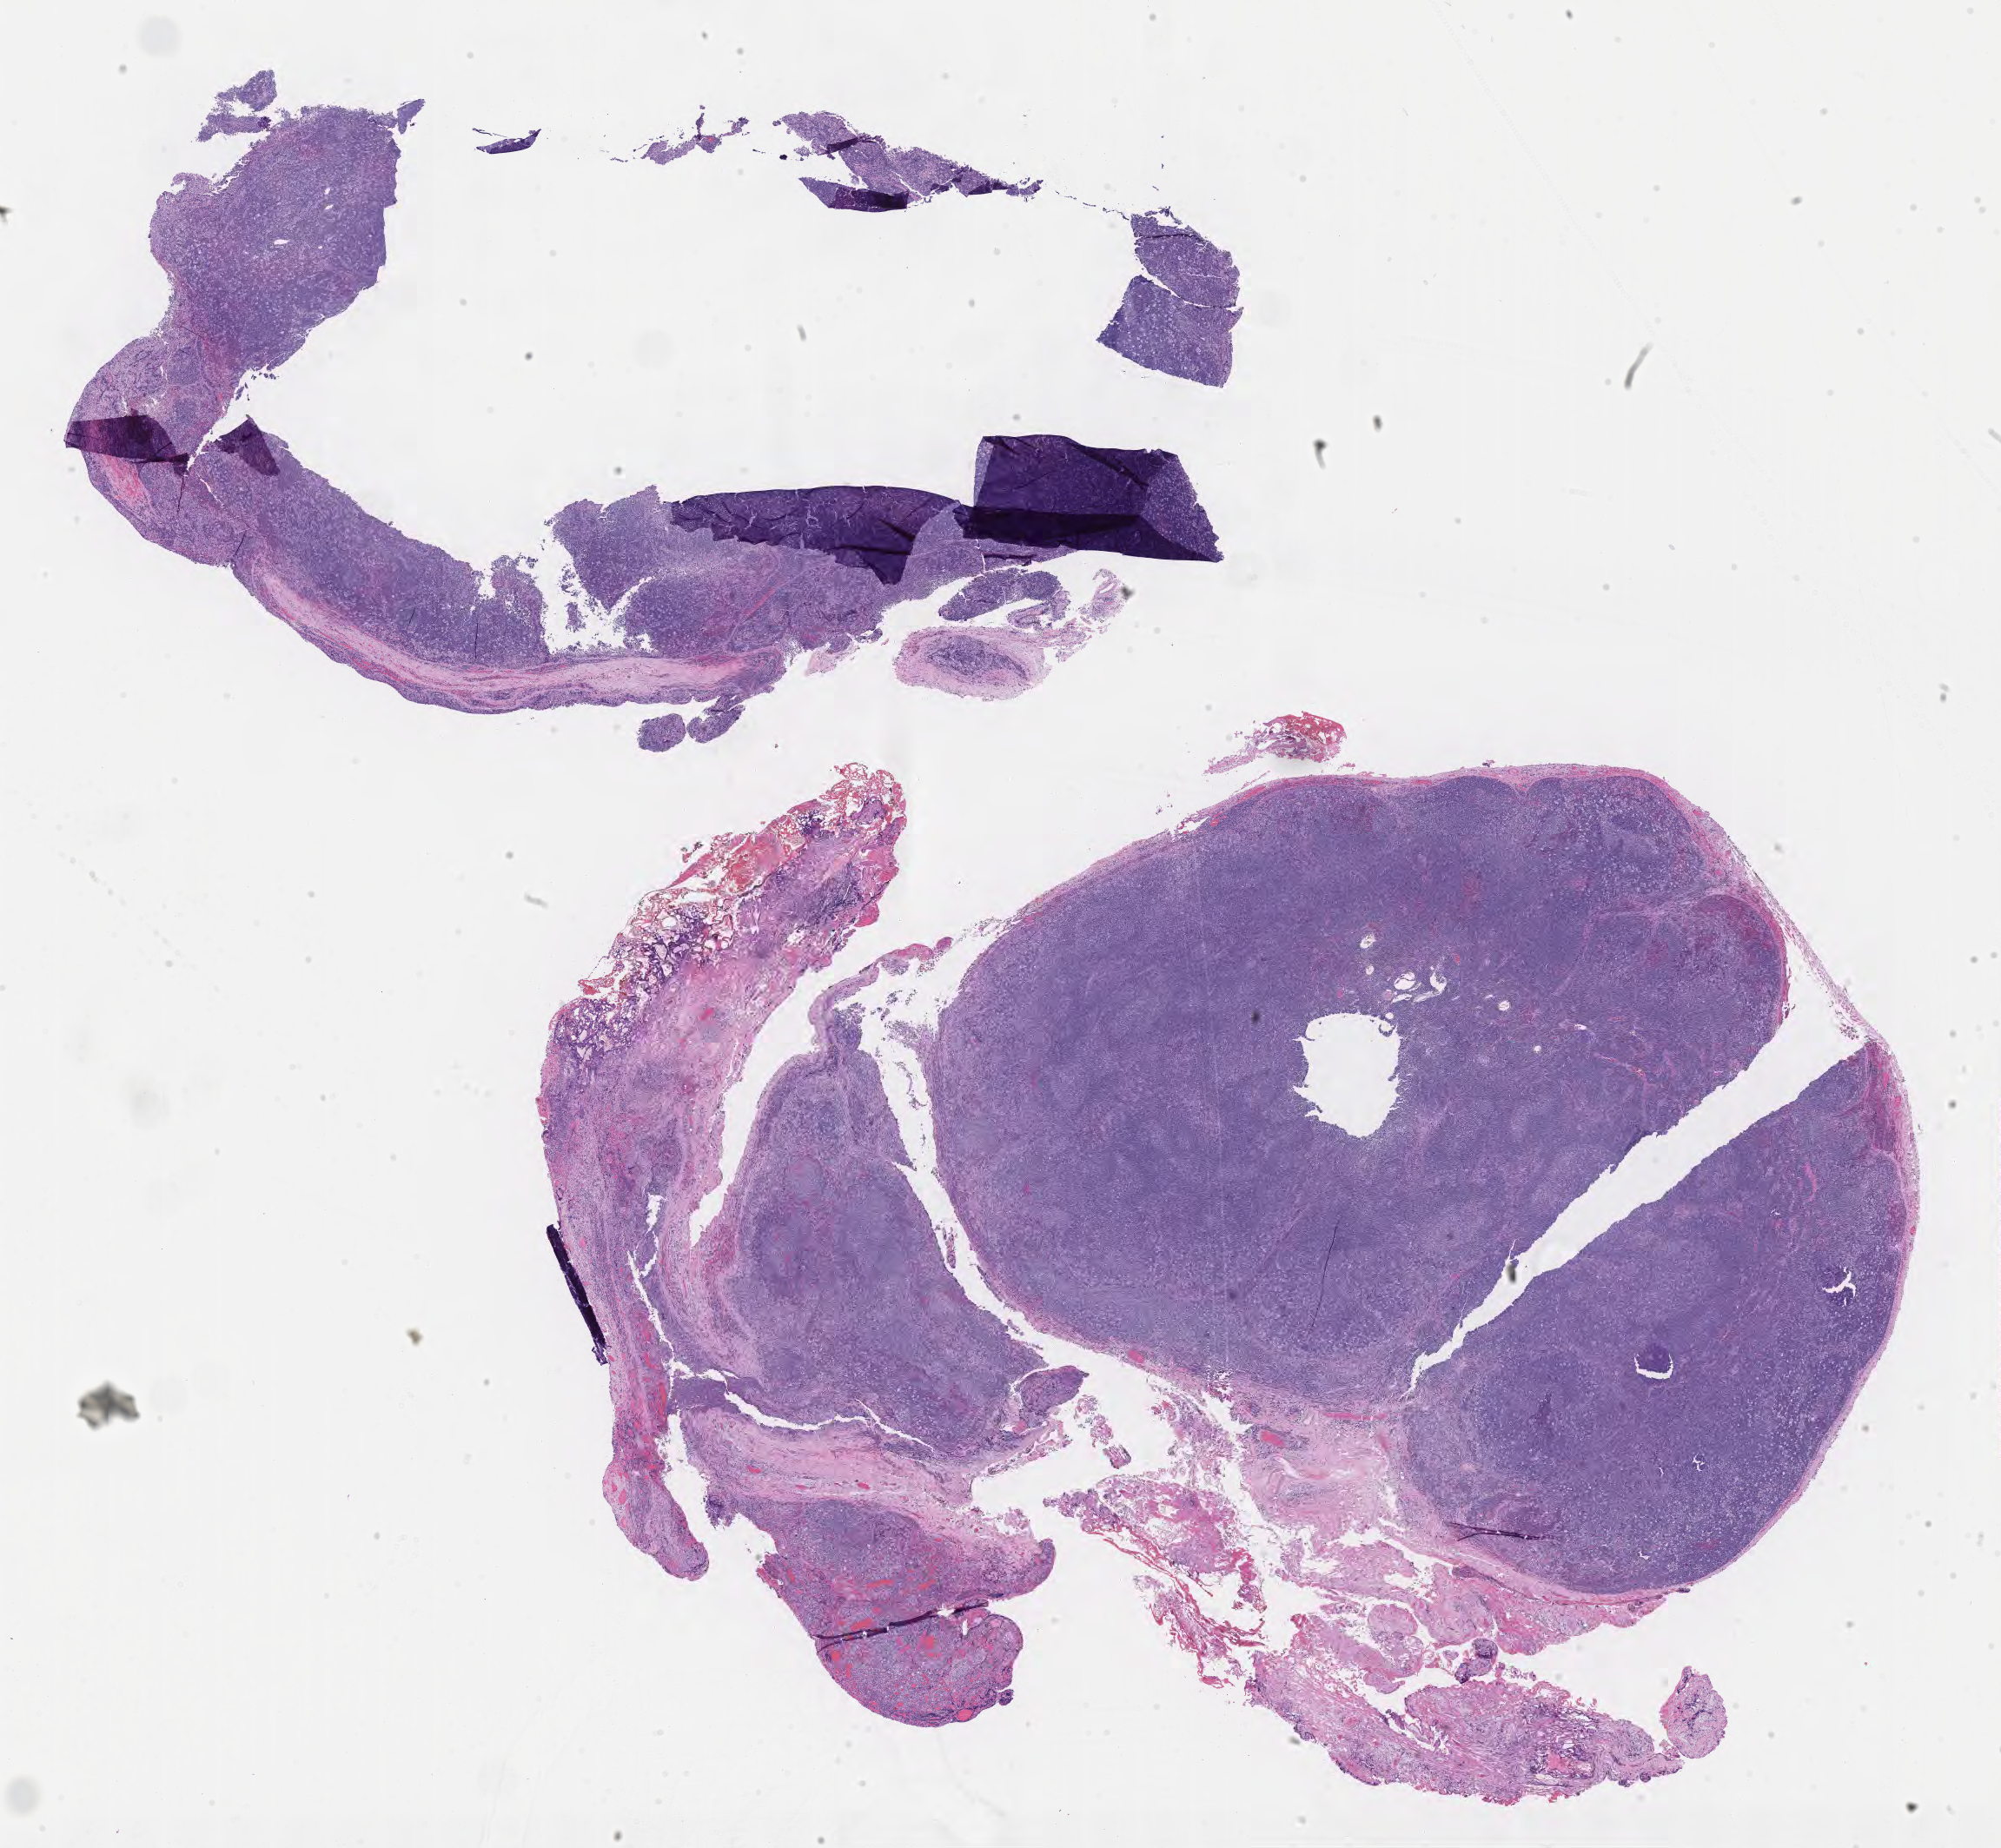
Hematoxylin and eosin (H&E) whole-slide image — whole scanned area (about 18.6 x 17.2 mm) shown as a low-resolution overview. Specimen: tumor tissue. Patient: male, age 25 years.
- histologic diagnosis: Burkitt lymphoma, NOS